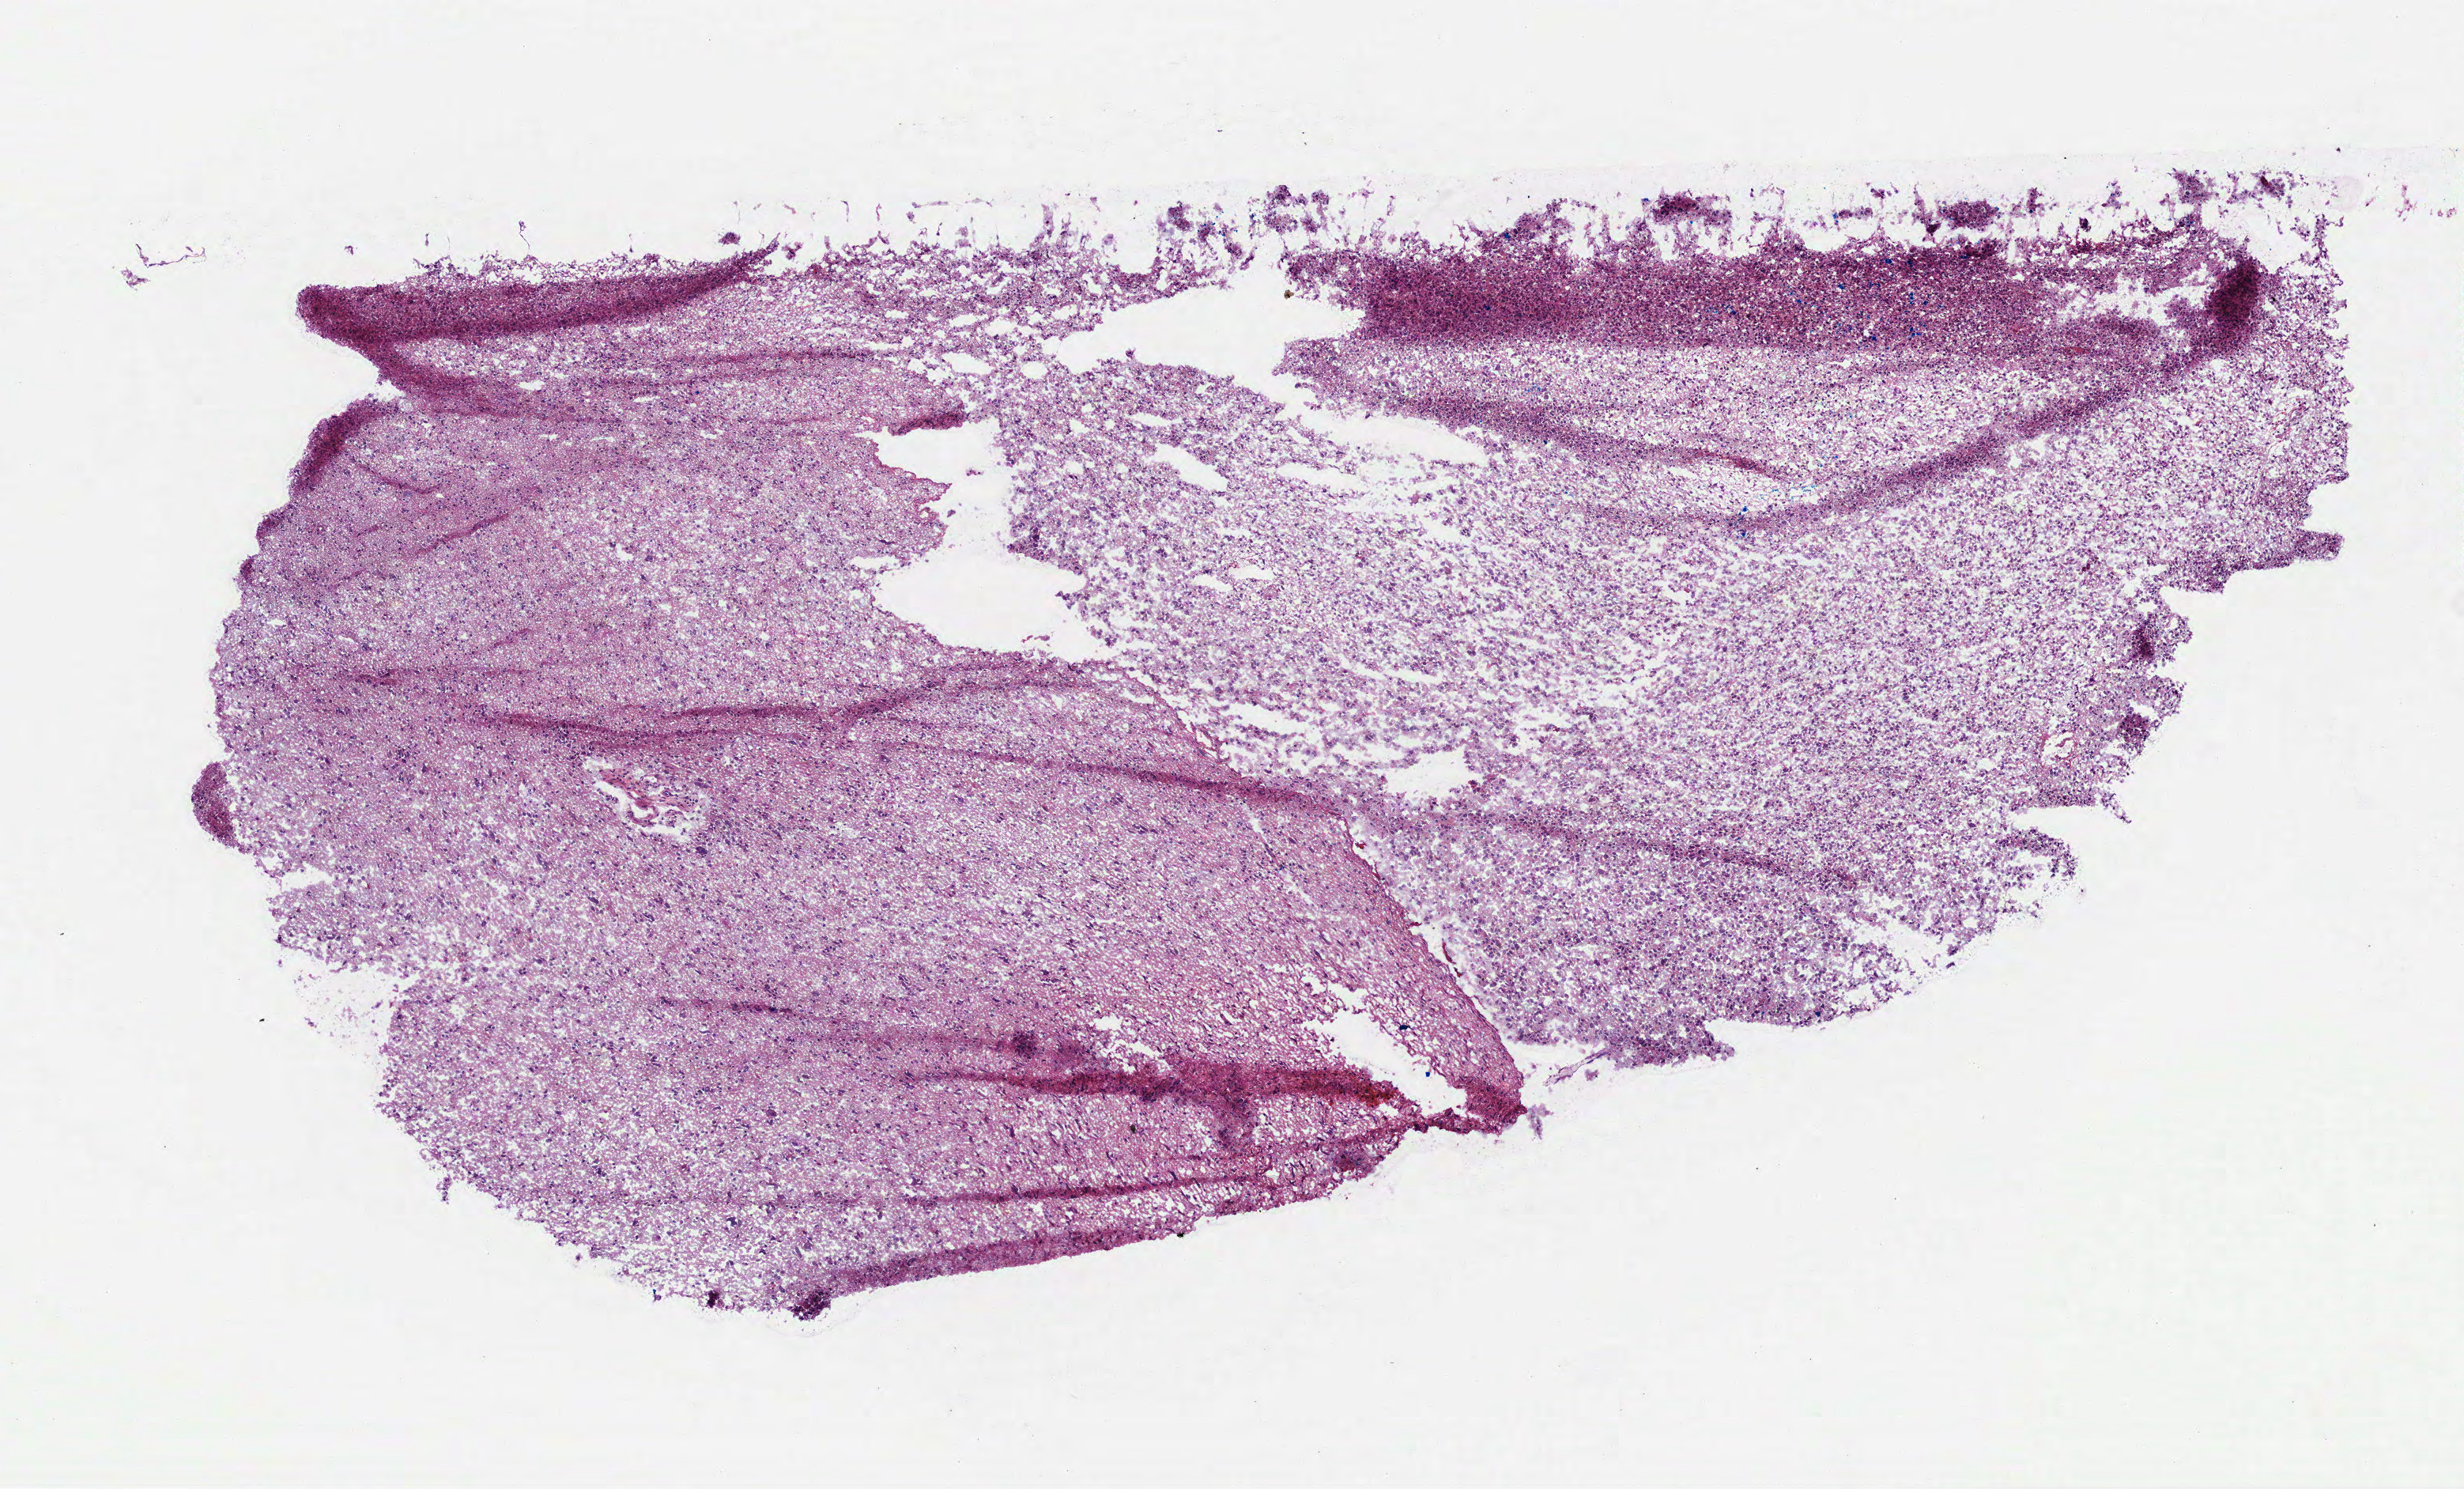
Digitized Hematoxylin and eosin (H&E) stained tissue section (whole slide), whole scanned area (about 6.3 x 3.8 mm) shown as a low-resolution overview, frozen section from the top of the tissue portion, brain, primary tumour sample. Female patient; age at initial diagnosis 45 years. Pathologist review of this section (percent, as recorded): tumour cells 100%, tumour nuclei 65%.
Histologic diagnosis: Astrocytoma, anaplastic.